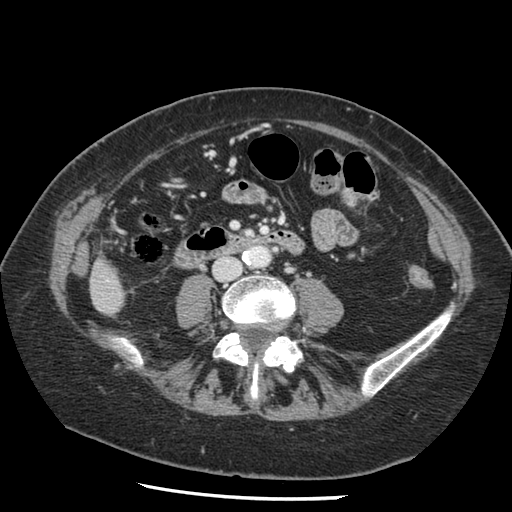
Contrast-enhanced abdominal CT, one axial slice. Position 17 of 148 along the scan axis. Reconstruction kernel STANDARD. 120 kVp. Intravenous contrast given. Soft-tissue window (W 400 / L 40 HU). 512 × 512 image matrix, field of view 330 × 330 mm. Female patient, age 85 years. Case-level facts recorded for this patient, not image findings: diagnosis: colorectal cancer liver metastases, imaged before liver resection; multiple liver metastases: no; largest metastasis: 0.9 cm; disease in both lobes: no.
Structures marked on this image (manually delineated by an expert):
- liver: bounding box [x1, y1, x2, y2] px = [91, 262, 124, 315]
- planned liver remnant (the part of the liver to remain after resection): [91, 262, 124, 315]